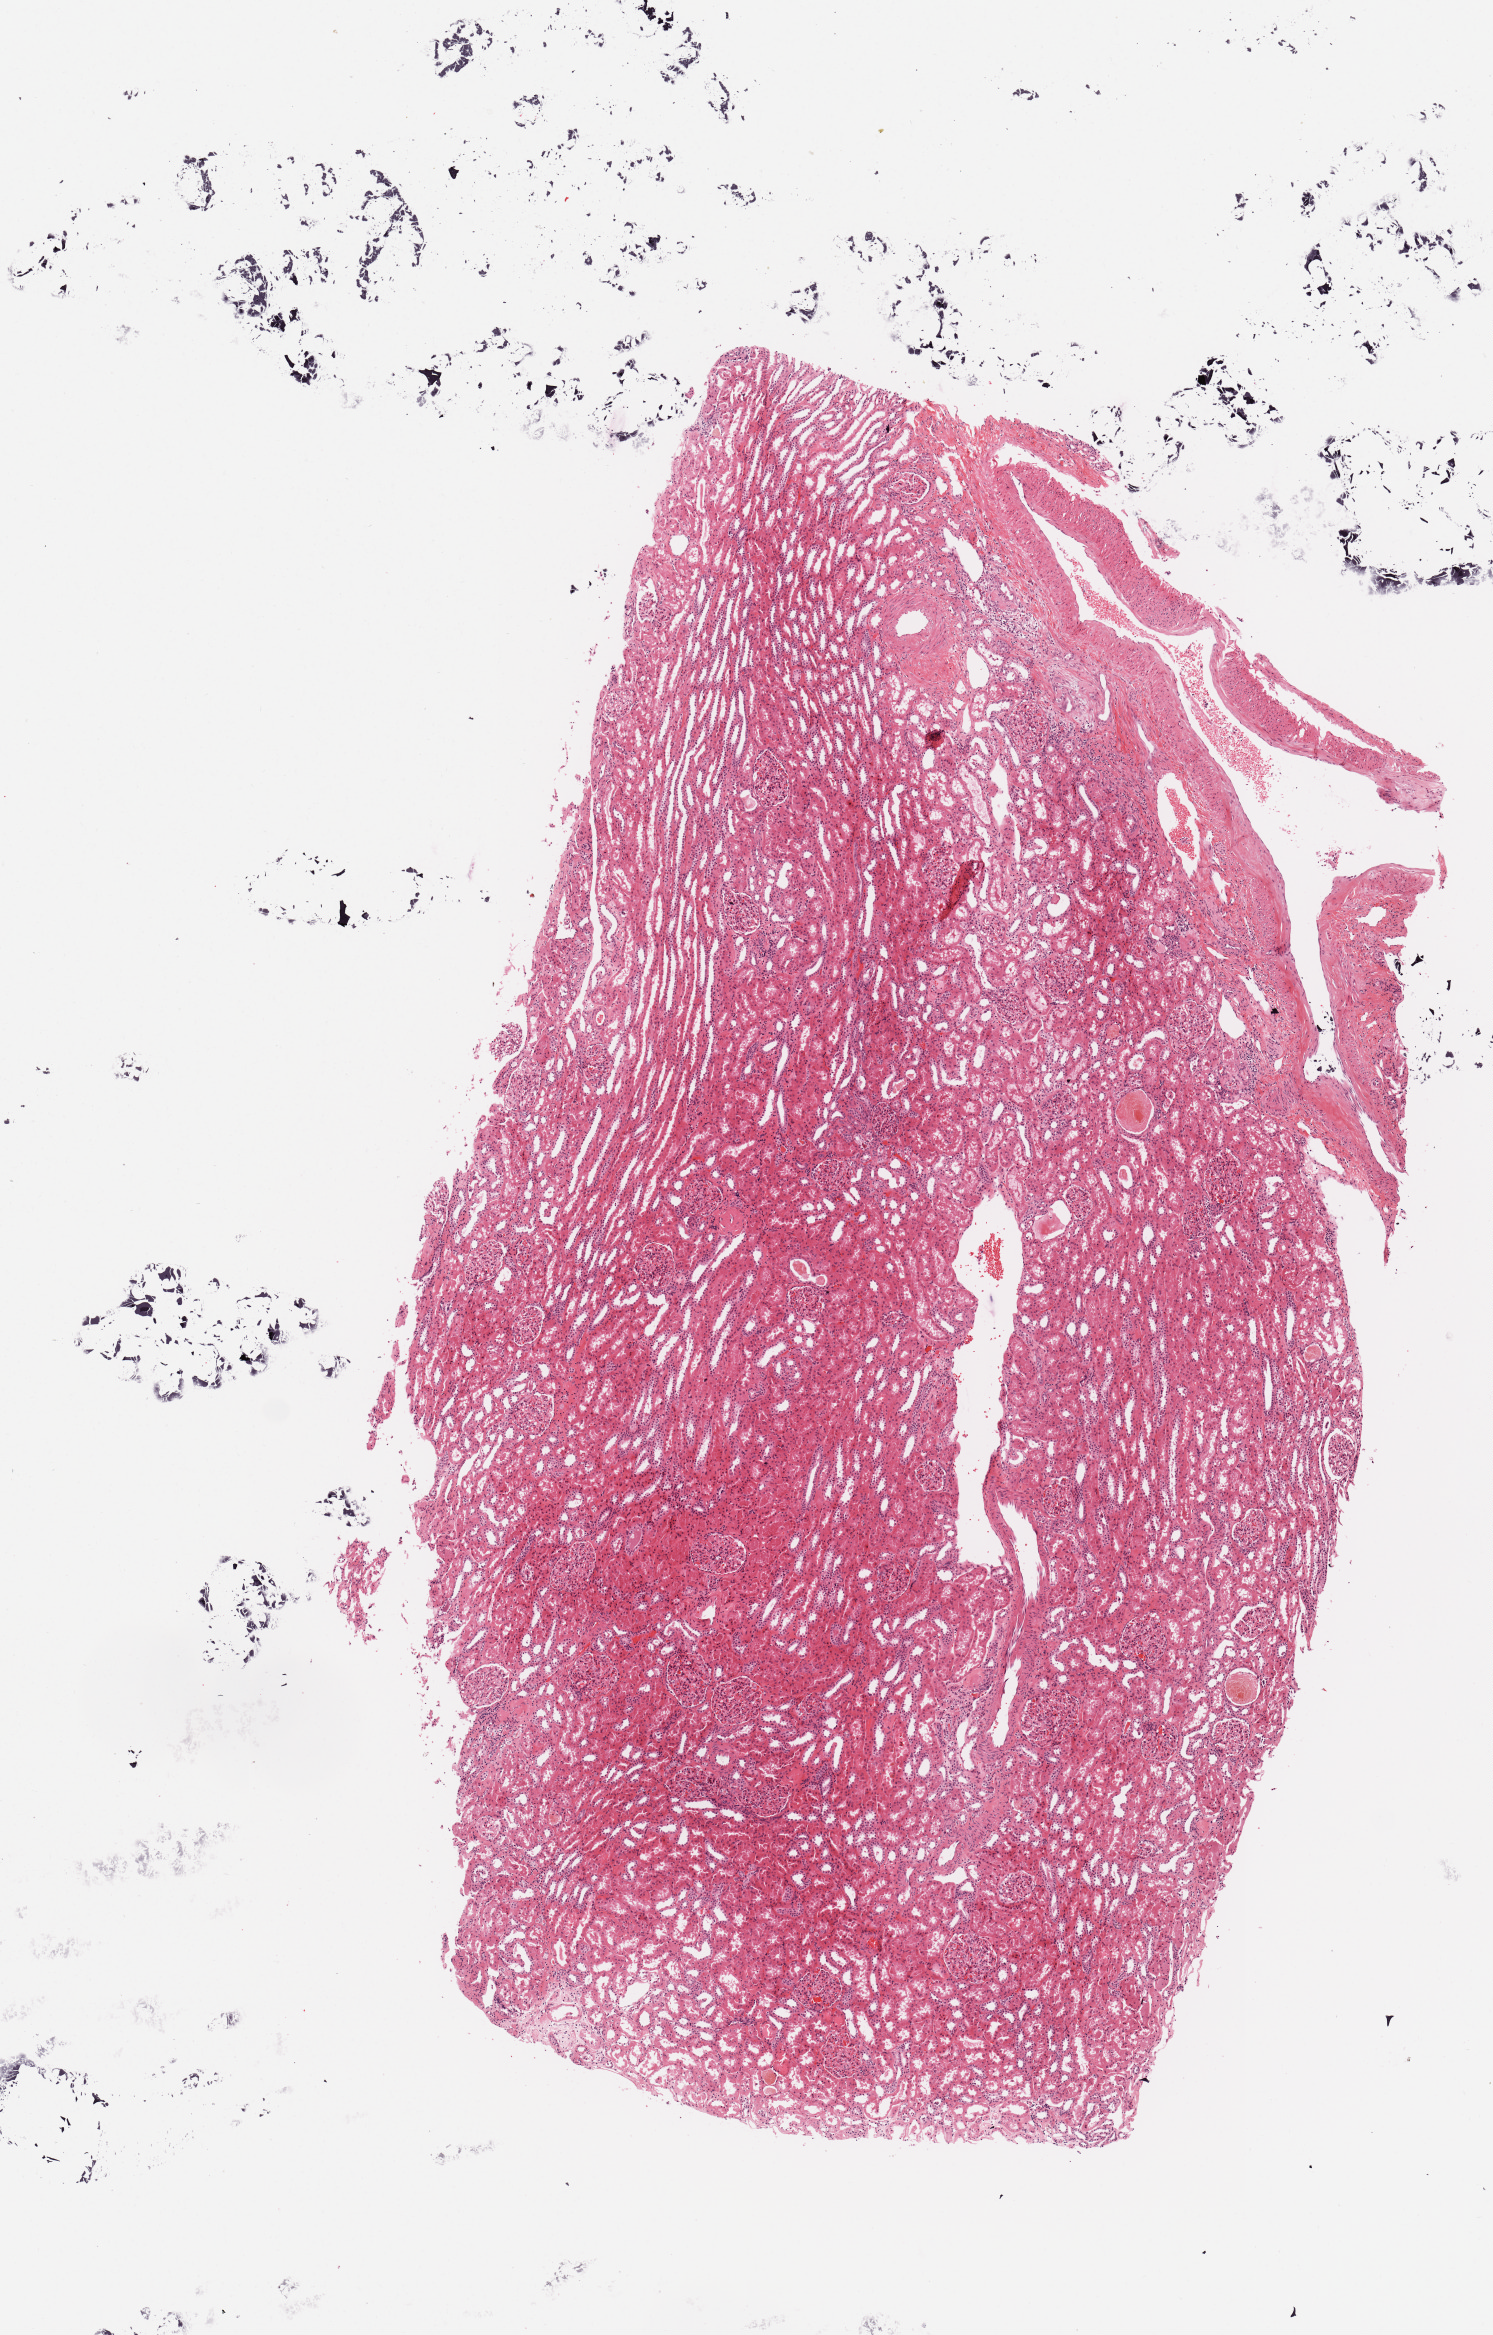
Whole-slide histology image, Hematoxylin and eosin (H&E) stained, shown as a low-resolution overview of the whole scanned area (about 5.9 x 9.2 mm); normal (non-tumour) tissue sample, sampled site: kidney. Male, 41 y/o.
This section: normal (non-tumour) tissue from the same patient. Patient diagnosis: Renal cell carcinoma, NOS.